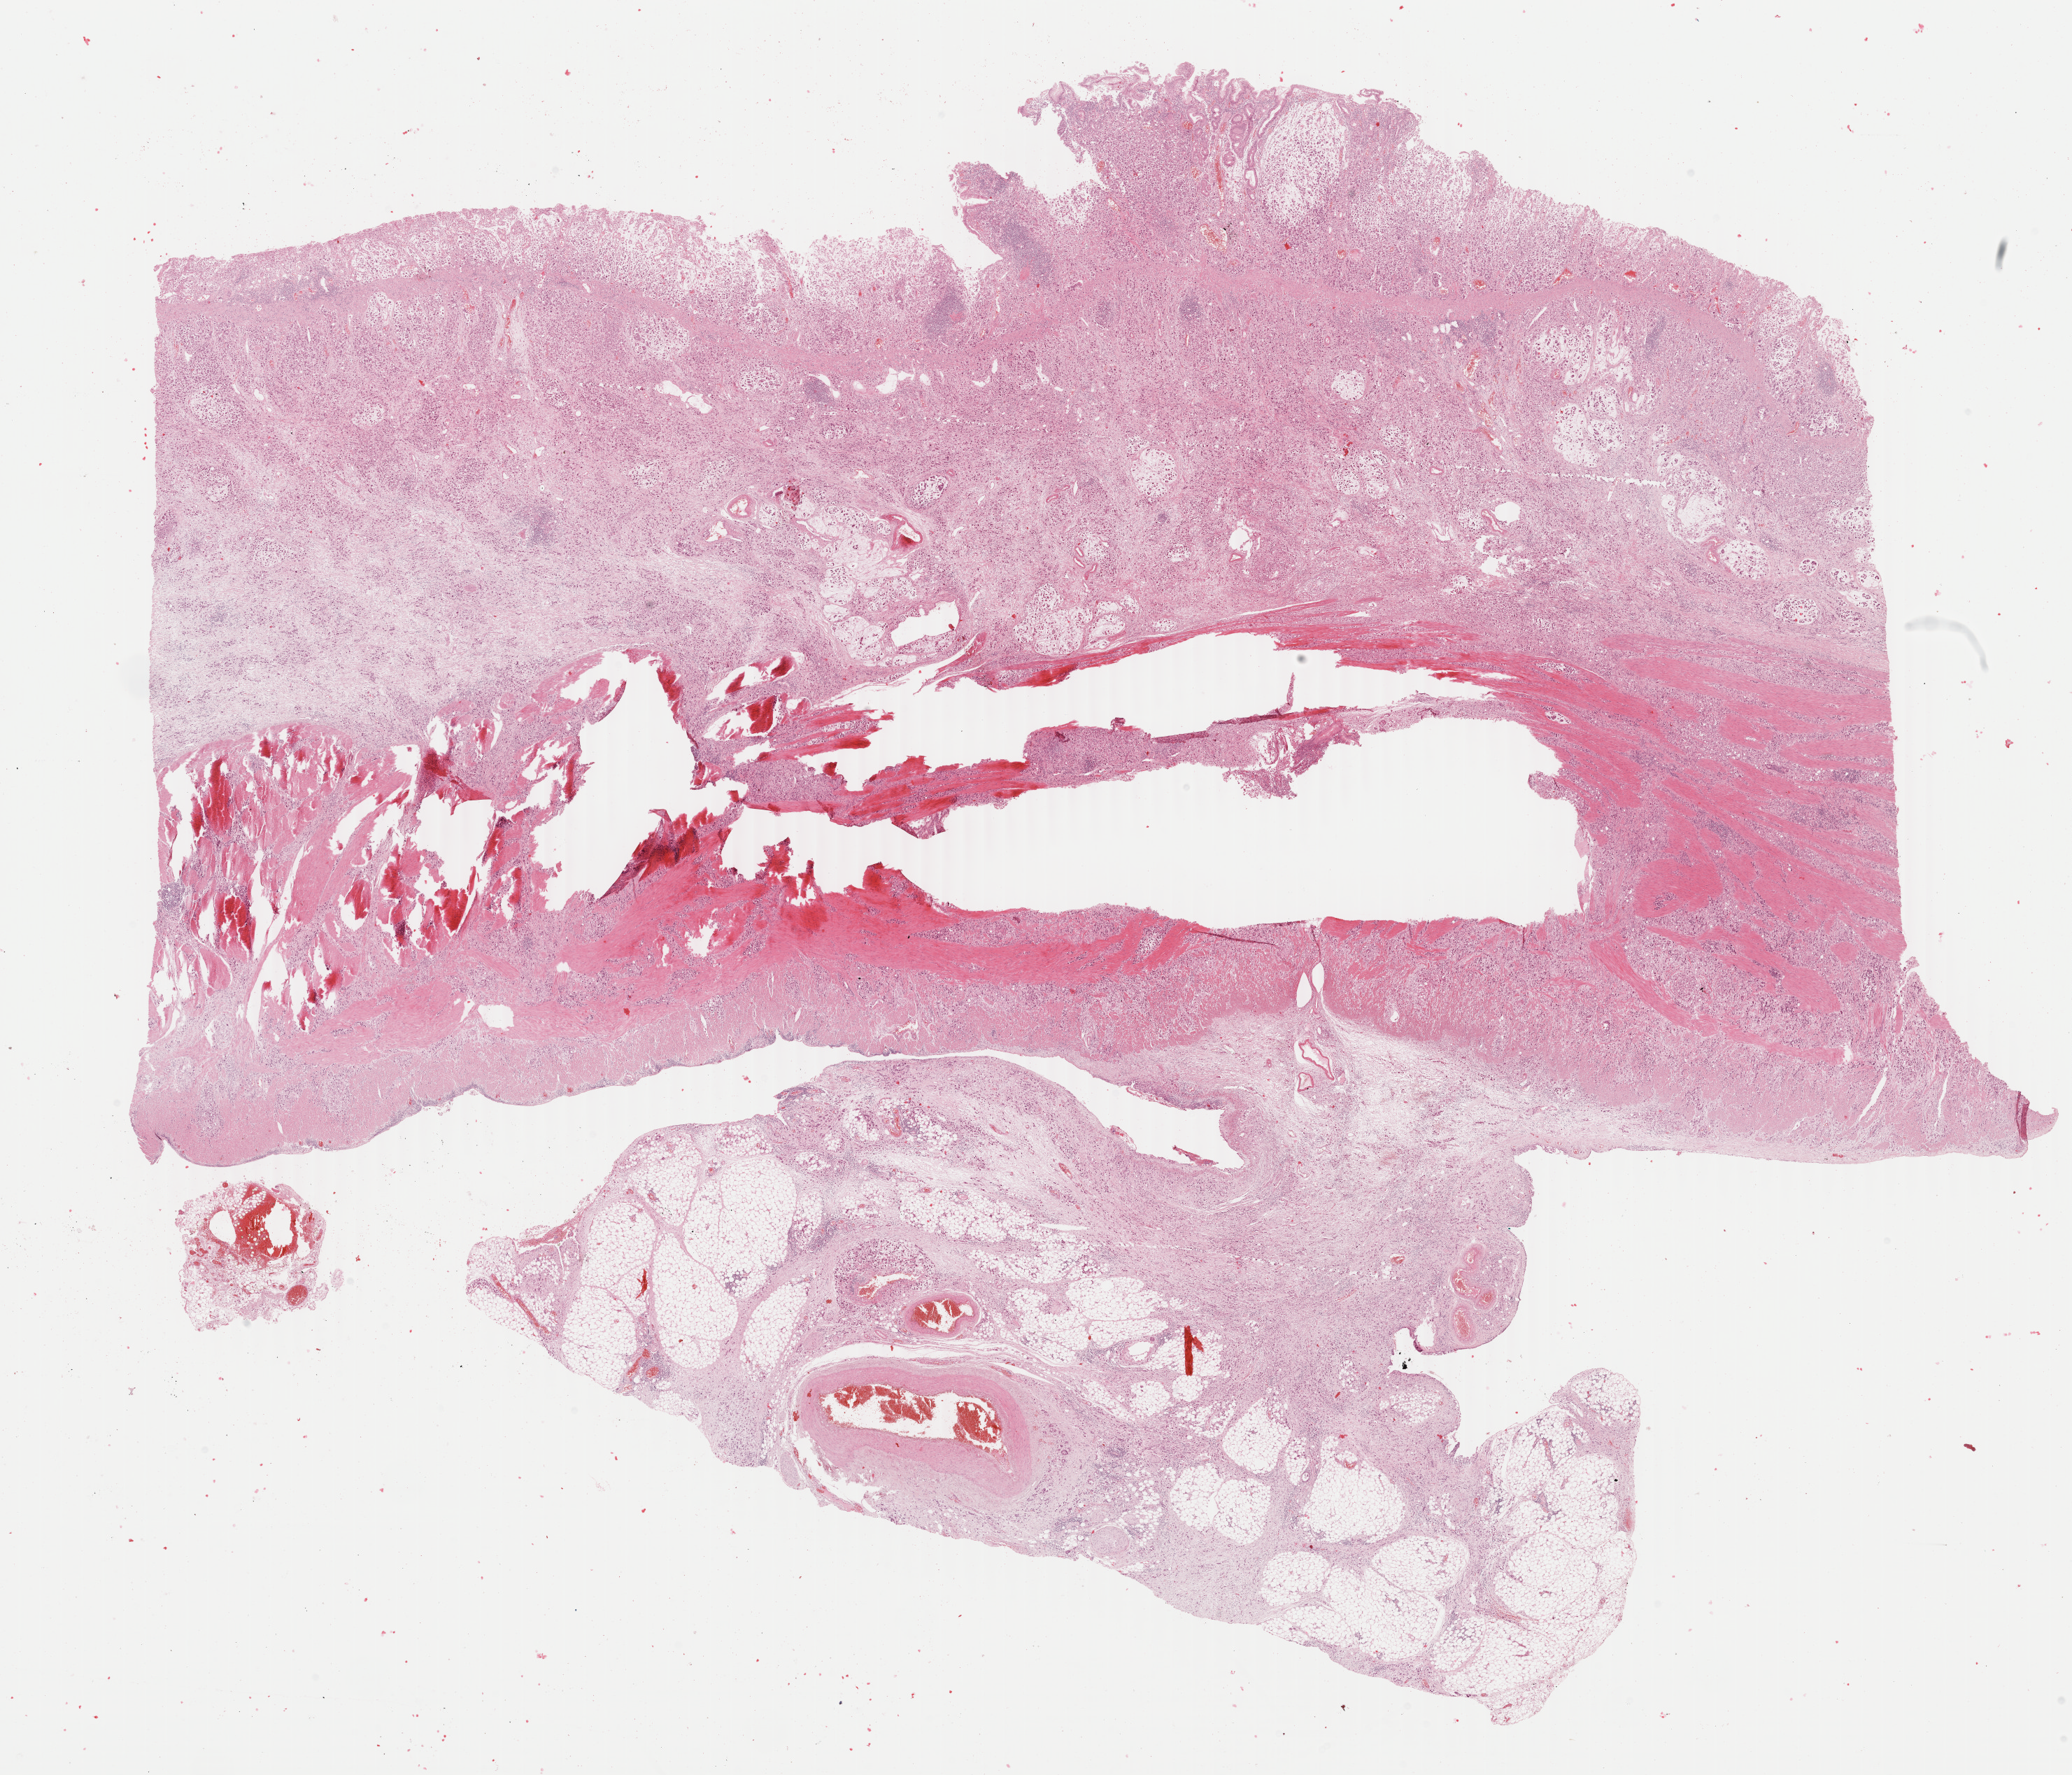
H&E-stained whole-slide image — shown as a low-resolution overview of the whole scanned area (about 23.6 x 20.2 mm), formalin-fixed paraffin-embedded (FFPE) diagnostic section, stomach, primary tumour sample. Male, age 74 years at initial diagnosis. Histologic grade: G3 (poorly differentiated).
Lymph nodes positive (case pathology): 11 of 12 examined. AJCC pathologic stage: IIIA (7th edition). Pathologic diagnosis: Mucinous adenocarcinoma (body of stomach).